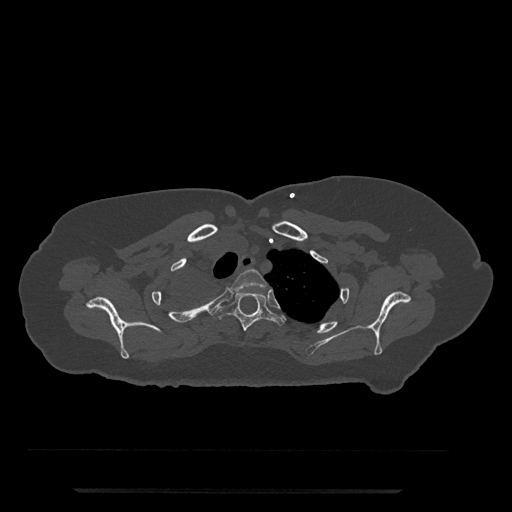
CT including the spine, one axial slice. Position 642 of 797 along the scan axis. Reconstruction kernel Br40s/3. 120 kVp. Bone window (W 1800 / L 400 HU). 0.5 mm slice thickness. 512 × 512 image matrix. Patient: female, 51 years. From the clinical record (not read from this slice): primary cancer: neuro; vertebrae with lytic lesions (as recorded): T8.
Annotated regions visible in this slice (semi-automatically segmented with operator editing):
- T2 vertebra: bounding box [x1, y1, x2, y2] px = [231, 269, 267, 294]
- T3 vertebra: [213, 291, 286, 331]